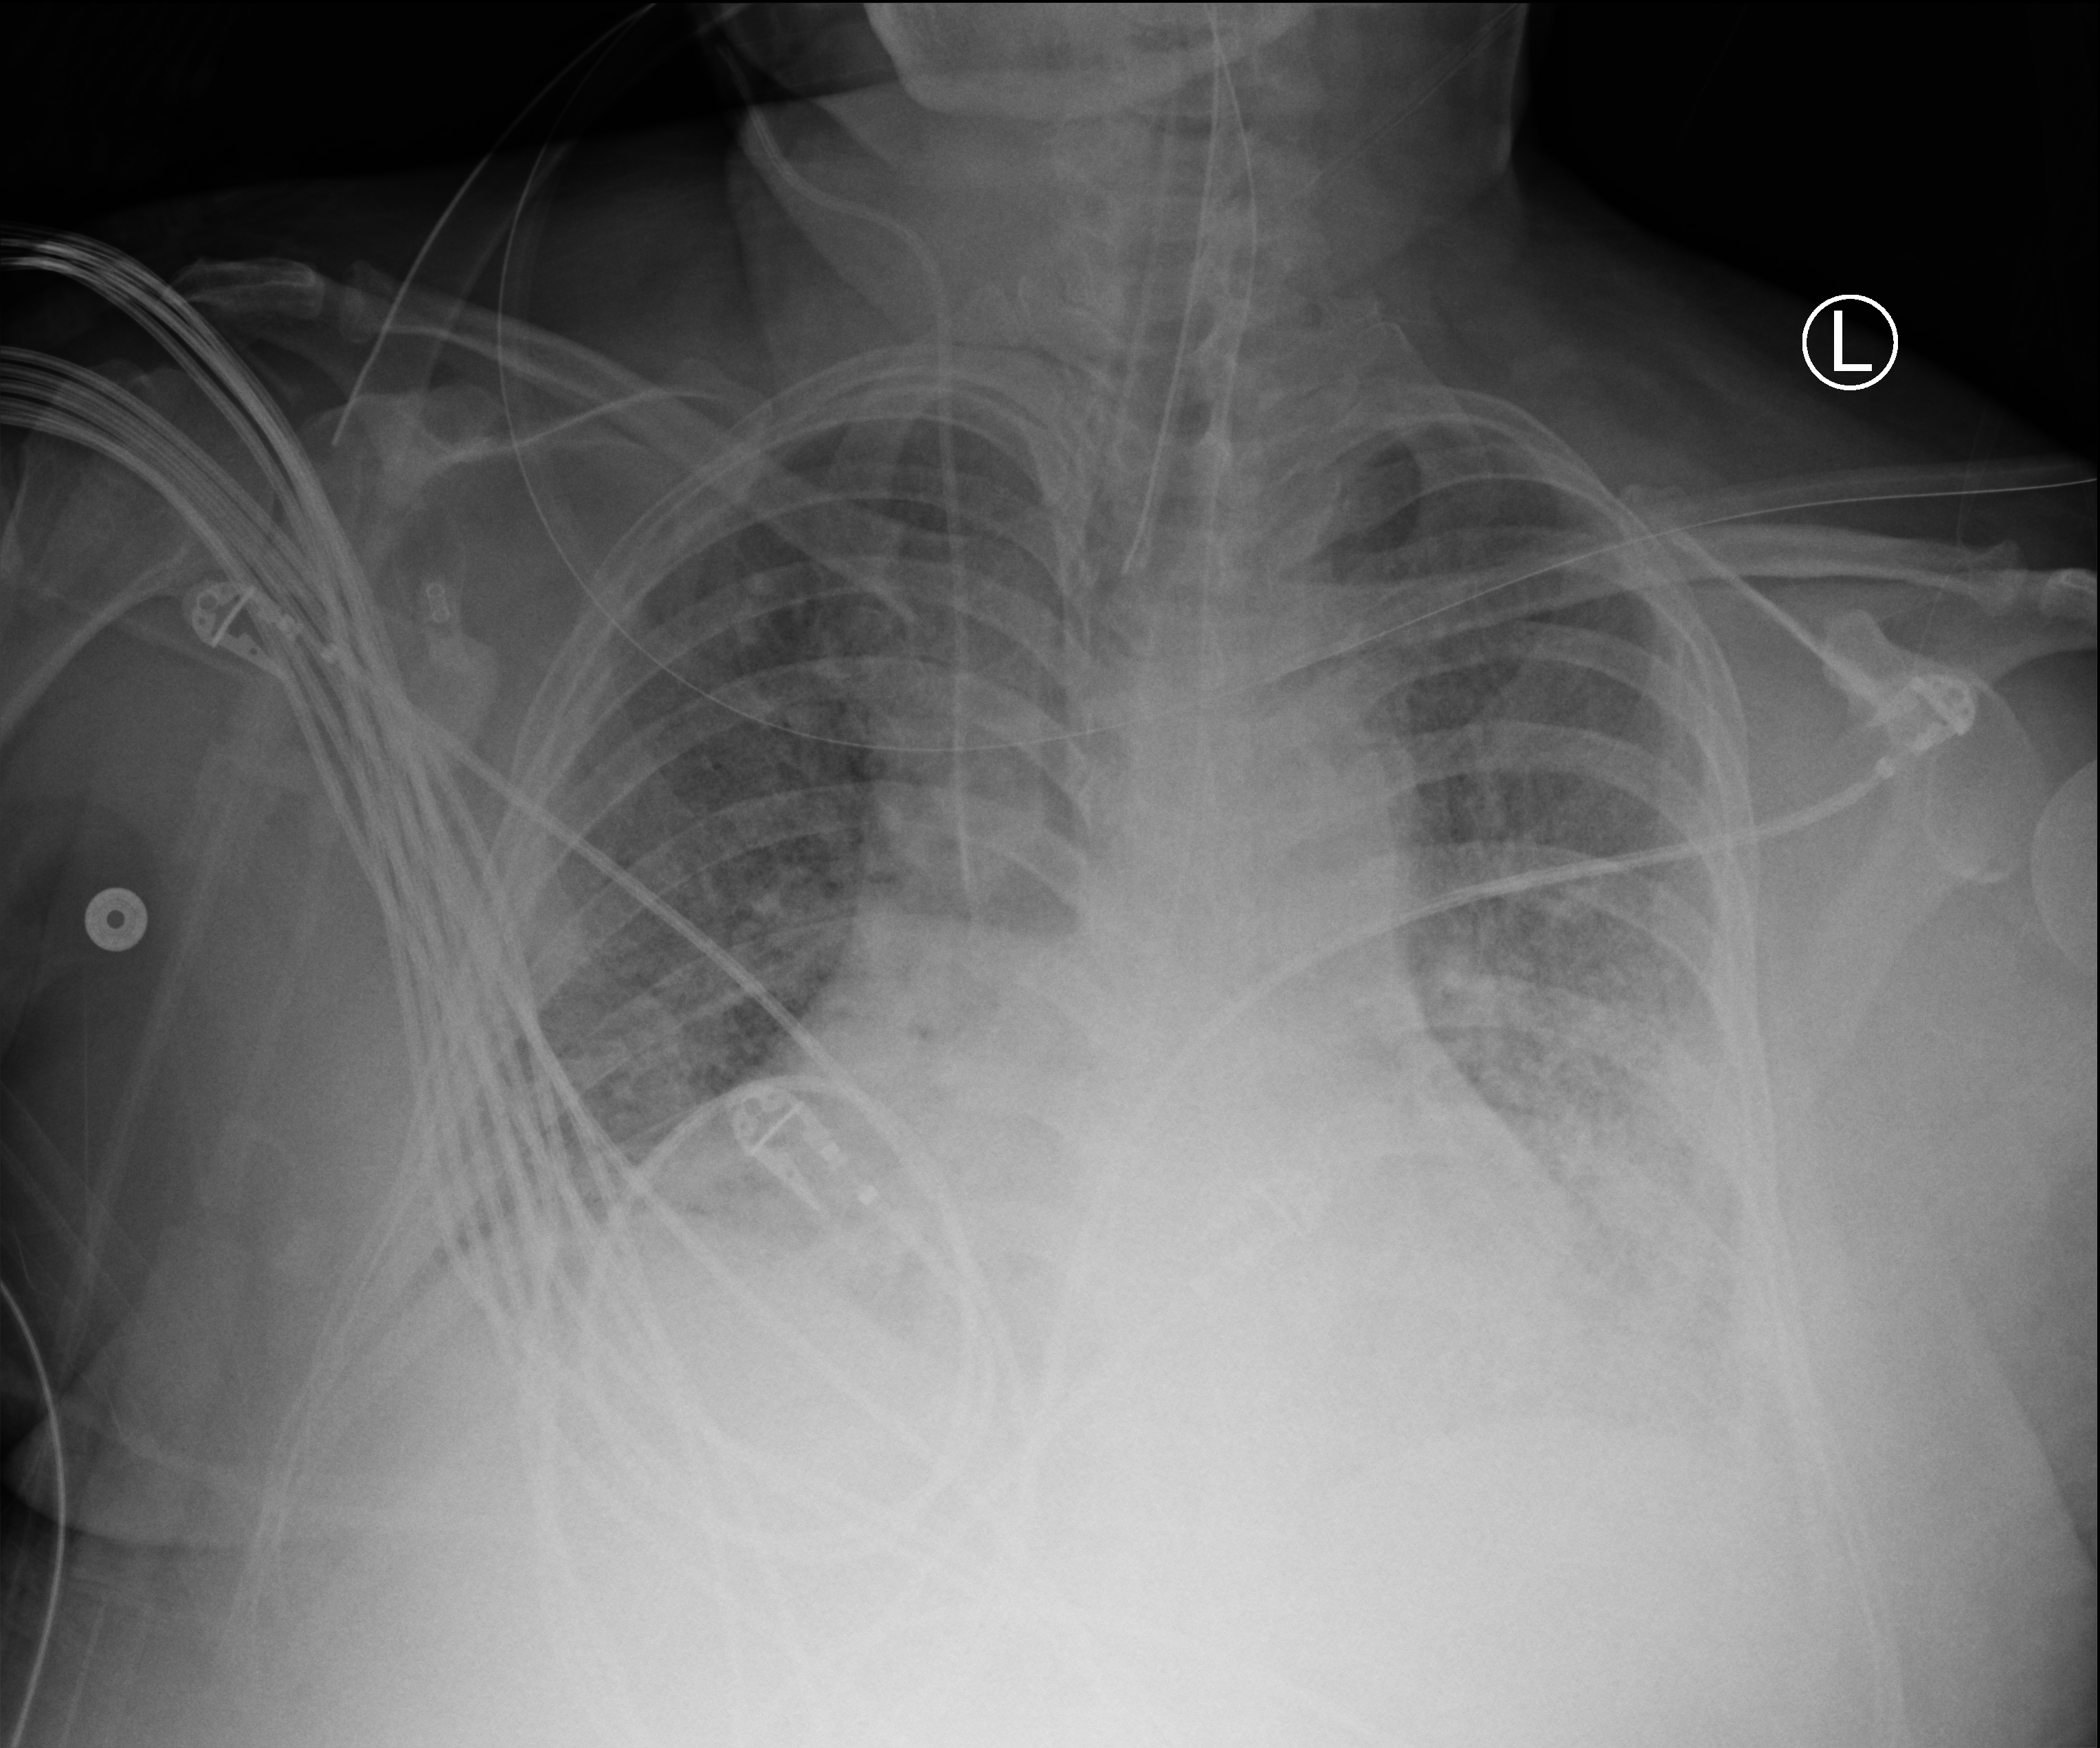
Chest X-ray (portable); anteroposterior (AP) projection. Patient hospitalised with COVID-19, aged 18–59 years.
Admission-level facts for this patient (not findings on this image; timing relative to this image not recorded):
- admitted to intensive care during this hospital stay: yes
- length of hospital stay: 48 days
- mechanically ventilated during this hospital stay: yes